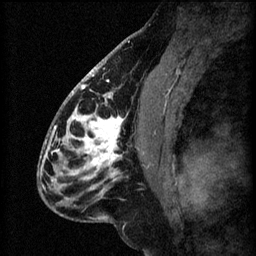
Breast MRI (dynamic contrast-enhanced), one sagittal slice; slice 33 of 60 in the series (ordered by position); 3 images stored at this slice position (order not interpretable as contrast timing); 1.5 T; TE 4.2 ms, TR 8.2 ms; 256 × 256 image matrix, field of view 180 × 180 mm. Female patient, age 41 years.
Annotated regions visible in this slice (semi-automatically segmented with operator editing):
- analysis volume of interest (the breast-tissue region the enhancement analysis was run in; not a lesion): bounding box [x1, y1, x2, y2] px = [56, 104, 157, 207]
- tumour enhancement mask (voxels above the 70 % enhancement threshold inside the analysis volume of interest): [56, 104, 144, 199]